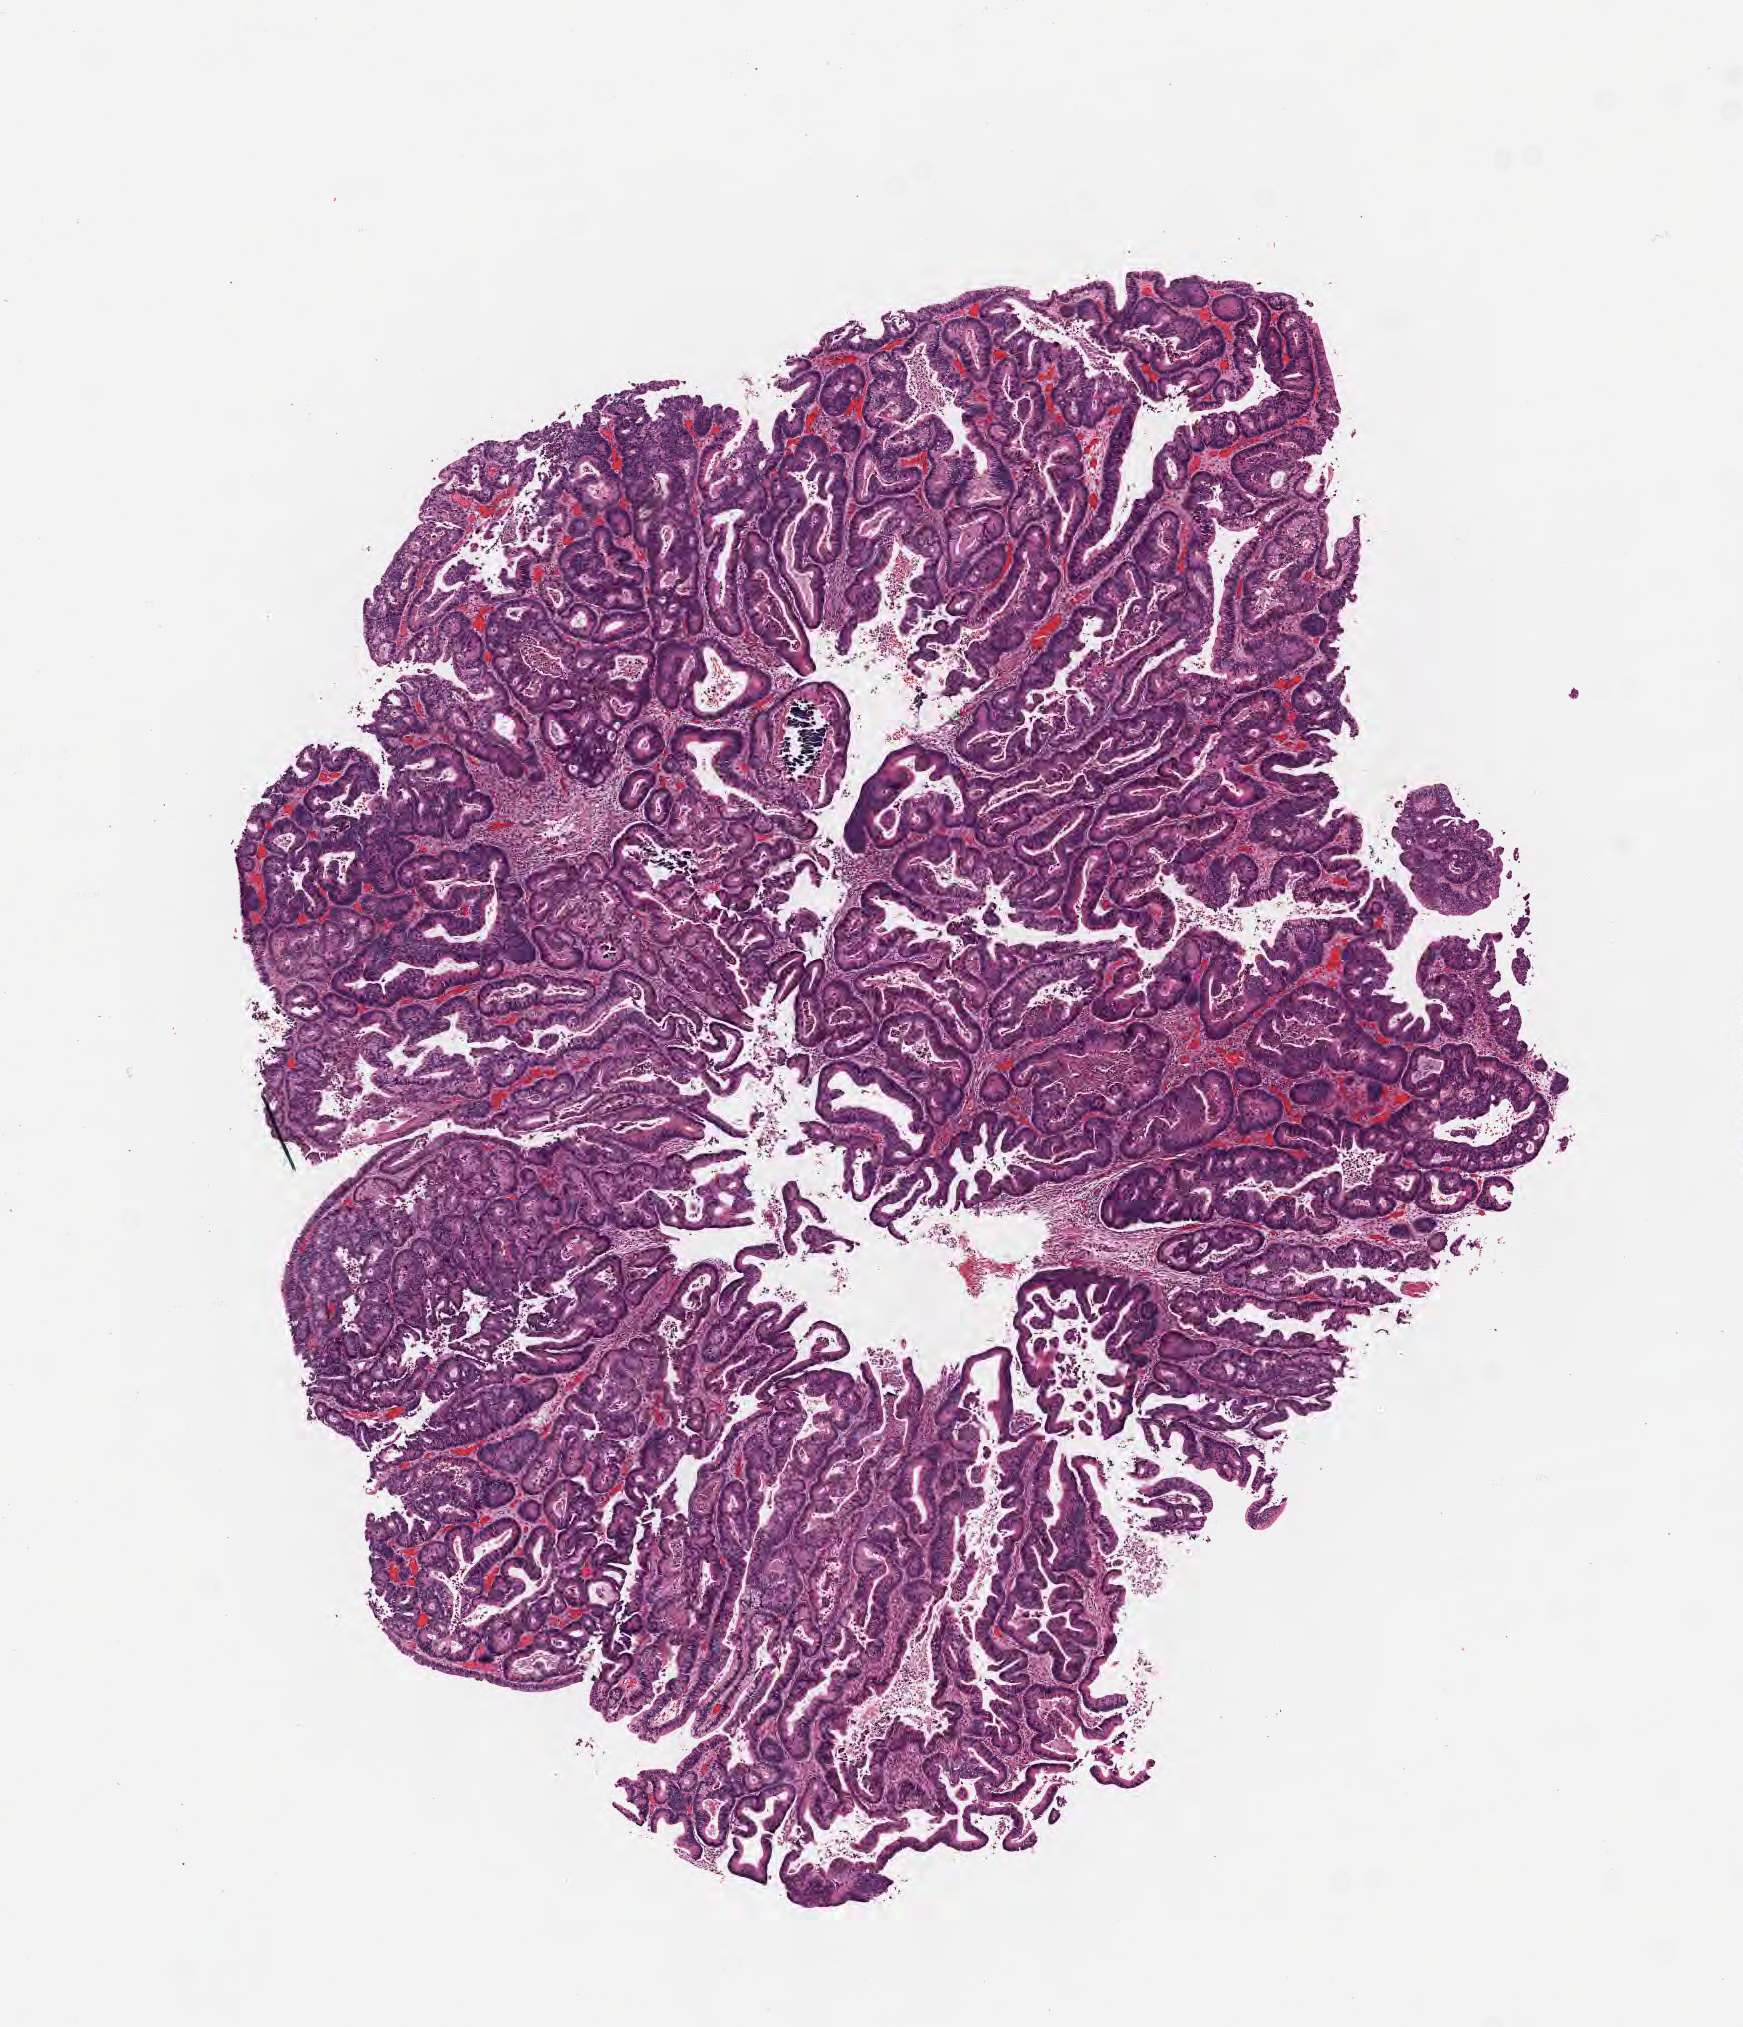
H&E whole-slide image — whole scanned area (about 7.0 x 8.2 mm) shown as a low-resolution overview; FFPE section; specimen: primary tumor; site: sigmoid colon. Male patient; age at initial diagnosis 68 years. Tumor grade: GB (borderline). Pathologist review of this section (percent, as recorded): tumor cells 70%, tumor nuclei 70%, stromal cells 30%, necrosis 0%, normal cells 0%. Infiltration values recorded for this section: lymphocyte infiltration 0%, monocyte infiltration 0%, neutrophil infiltration 0%.
Diagnosis: Adenocarcinoma, NOS. AJCC pathologic stage: Stage IVA. Section: top of the tissue portion.